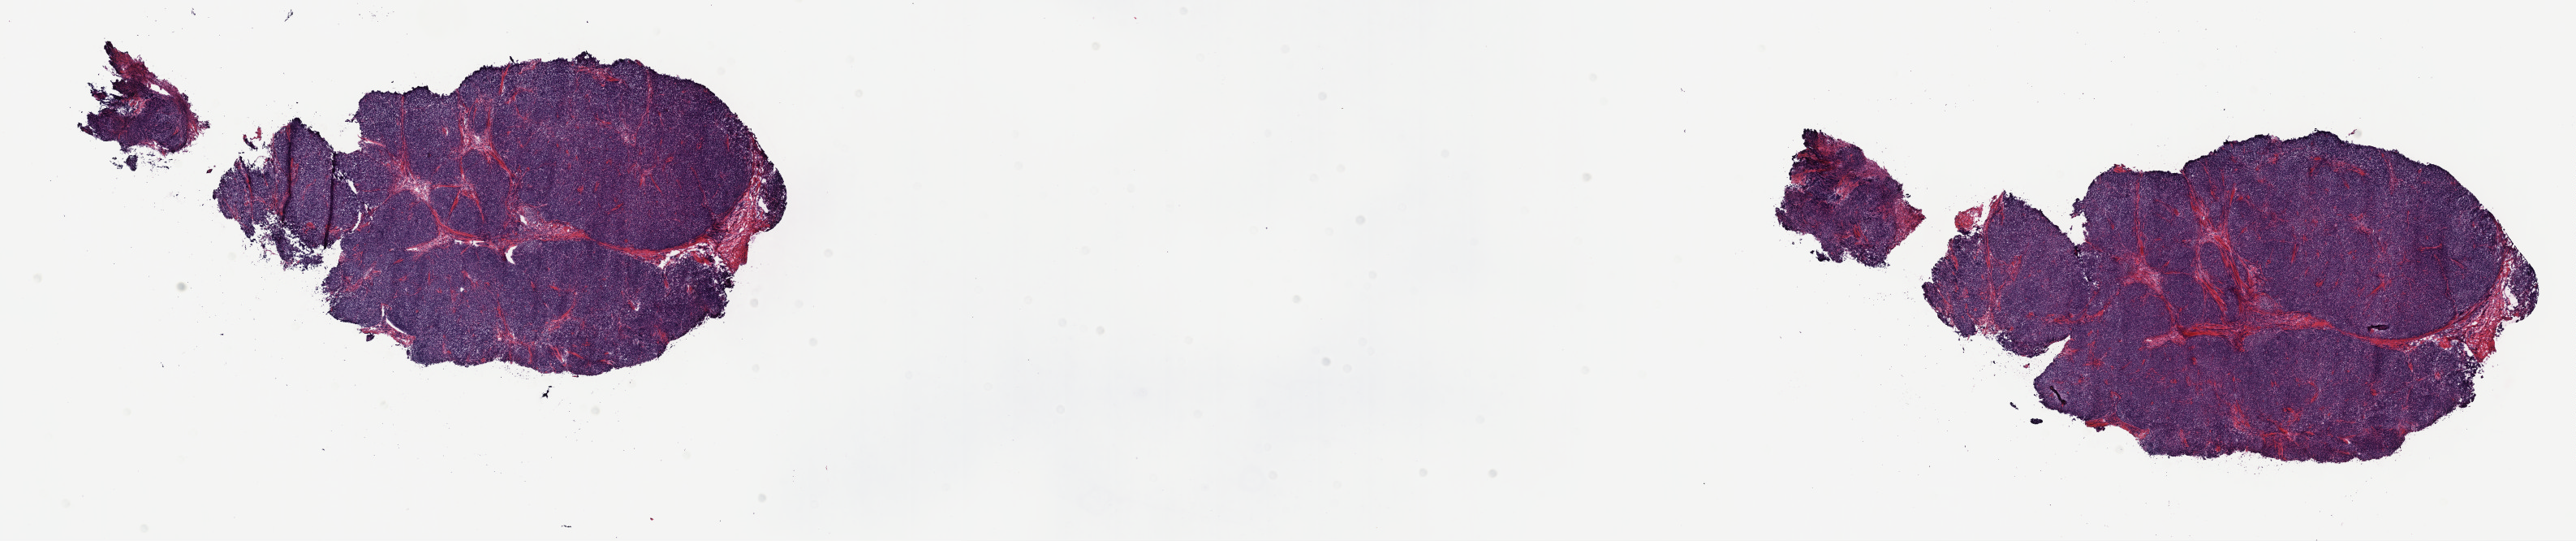
Whole-slide histology image, H&E, shown as a low-resolution overview of the whole scanned area (about 25.7 x 5.4 mm), frozen section from the top of the tissue portion, sample: primary tumour, thymus. Patient: female, age at initial diagnosis 51 years. Slide review estimates, as recorded: tumour cells 85%, tumour nuclei 85%, normal cells 0%, stromal cells 15%, necrosis 0%. Infiltration values recorded for this section: lymphocyte infiltration 2%, monocyte infiltration 1%, neutrophil infiltration 1%.
Histologic diagnosis: Thymoma, type AB, malignant.